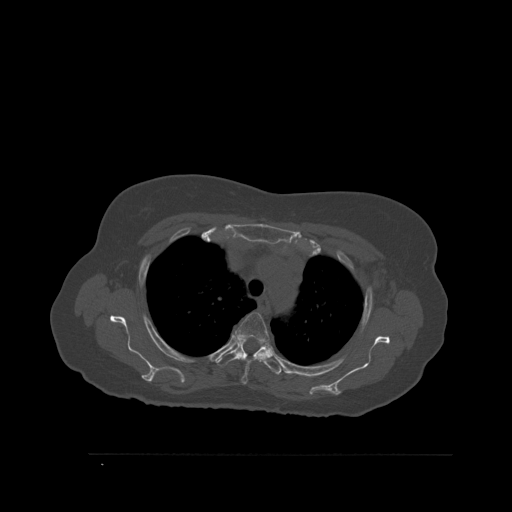
CT including the spine, one axial slice; slice 414 of 527 in the series (ordered by position); bone window (W 1800 / L 400 HU); 512 × 512 image matrix. Female patient, age 73 years. From the clinical record (not read from this slice): primary cancer: breast.
Outlined on this slice (semi-automatic segmentation, software-assisted and operator-edited):
- T3 vertebra: bounding box <235,312,270,385> (left, top, right, bottom; pixels)
- T4 vertebra: <217,337,281,375>